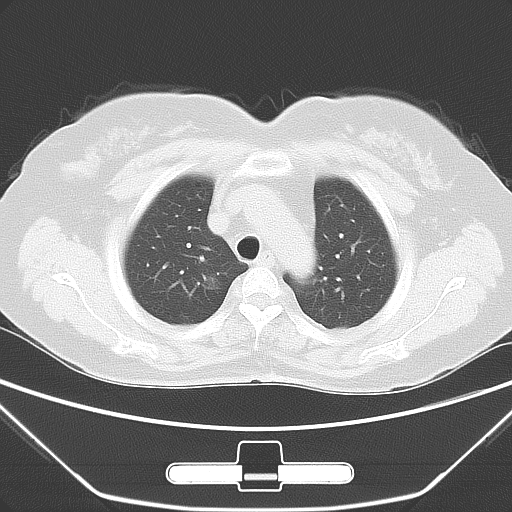
Chest CT, one axial slice. Slice 45 of 55 in the series (ordered by position). Lung window (W 1500 / L -600 HU). 5 mm slice thickness. 512 × 512 image matrix, field of view 356 × 356 mm. Patient: female, 63 years. From the clinical record (not read from this slice): clinical TNM (as recorded): T1a N0 M0.
Structures marked on this image (bounding box drawn by a radiologist):
- lung tumour (recorded histology: adenocarcinoma): bounding box <198,269,231,301> (left, top, right, bottom; pixels)